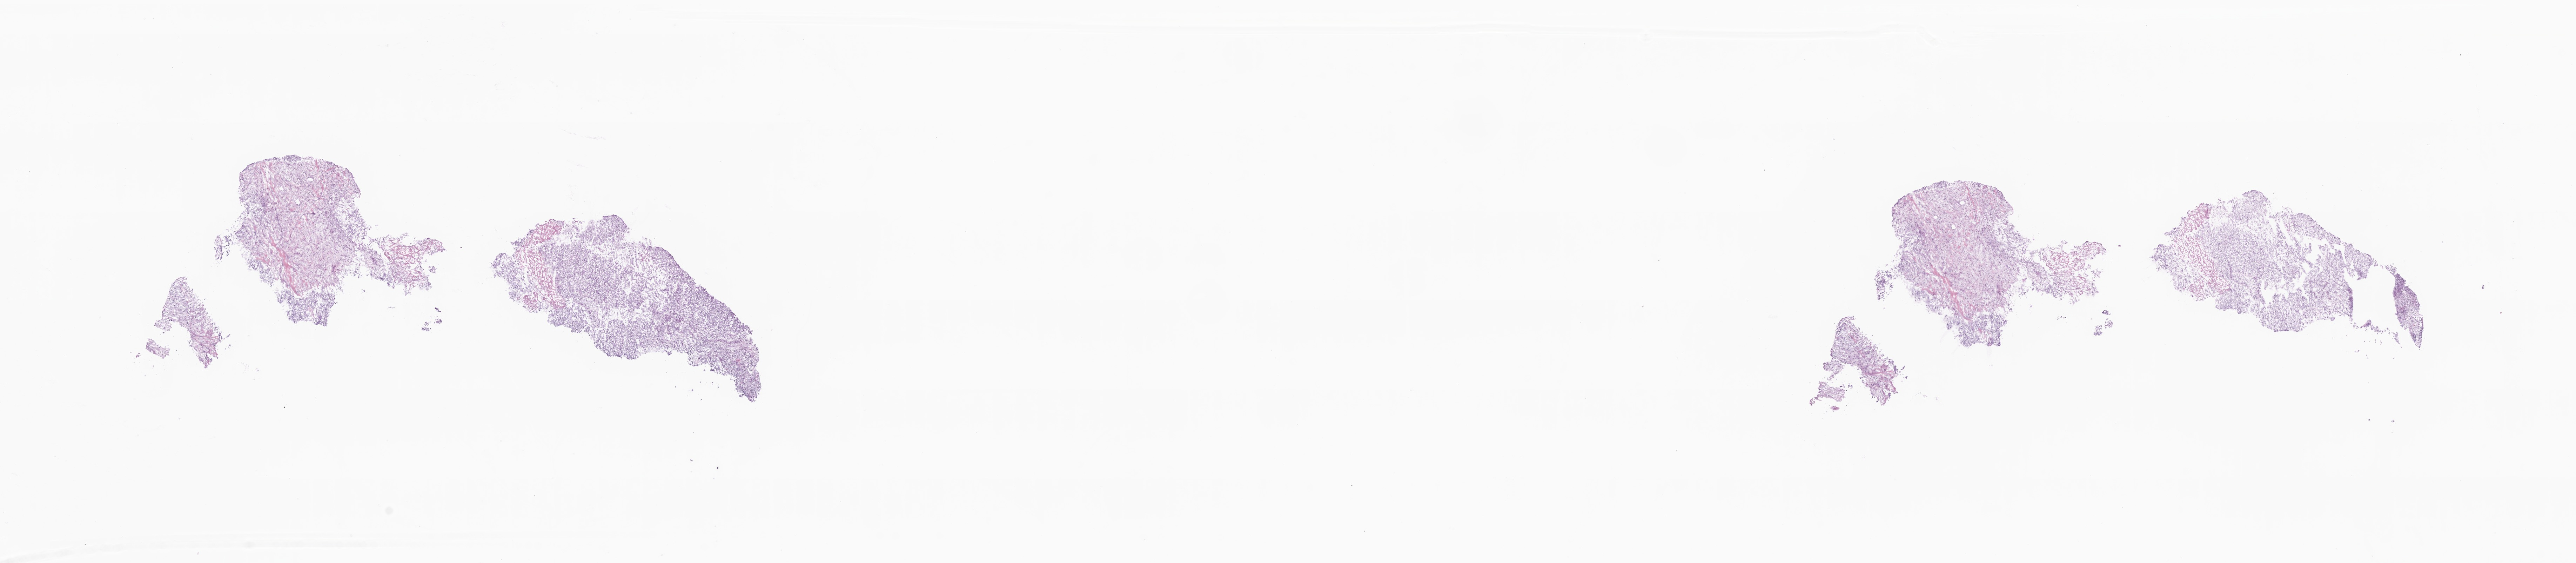
Whole-slide image, haematoxylin and eosin stain — low-resolution overview of the scanned area, about 31.0 x 6.8 mm; frozen section (tissue freezing medium); primary tumor; site: breast (left). Female, age 45 years at initial diagnosis. Composition of this section per pathologist review: tumor cells 60%, tumor nuclei 80%, stromal cells 25%, necrosis 15%, normal cells 0%. Infiltration values recorded for this section: lymphocyte infiltration 0%, monocyte infiltration 0%, neutrophil infiltration 0%.
* section: top of the tissue portion
* diagnosis: Infiltrating duct carcinoma, NOS